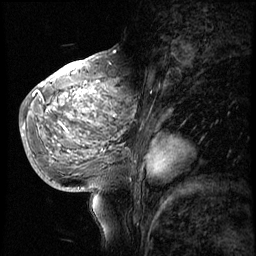
Breast MRI (dynamic contrast-enhanced), one sagittal slice; position 31 of 56 along the scan axis; 4 images stored at this slice position (order not interpretable as contrast timing); 1.5 T; TE 4.2 ms, TR 8.9 ms; 2.5 mm slice thickness; 256 × 256 image matrix, field of view 220 × 220 mm. Female patient, age 51 years. From the clinical record (not read from this slice): setting: breast cancer imaged before/during neoadjuvant chemotherapy; receptor status: triple-negative.
Annotated regions visible in this slice (semi-automatically segmented with operator editing):
- analysis volume of interest (the breast-tissue region the enhancement analysis was run in; not a lesion): box from (x=30, y=70) to (x=150, y=173) px
- tumour enhancement mask (voxels above the 140 % enhancement threshold inside the analysis volume of interest): (x=34, y=82)–(x=150, y=165)